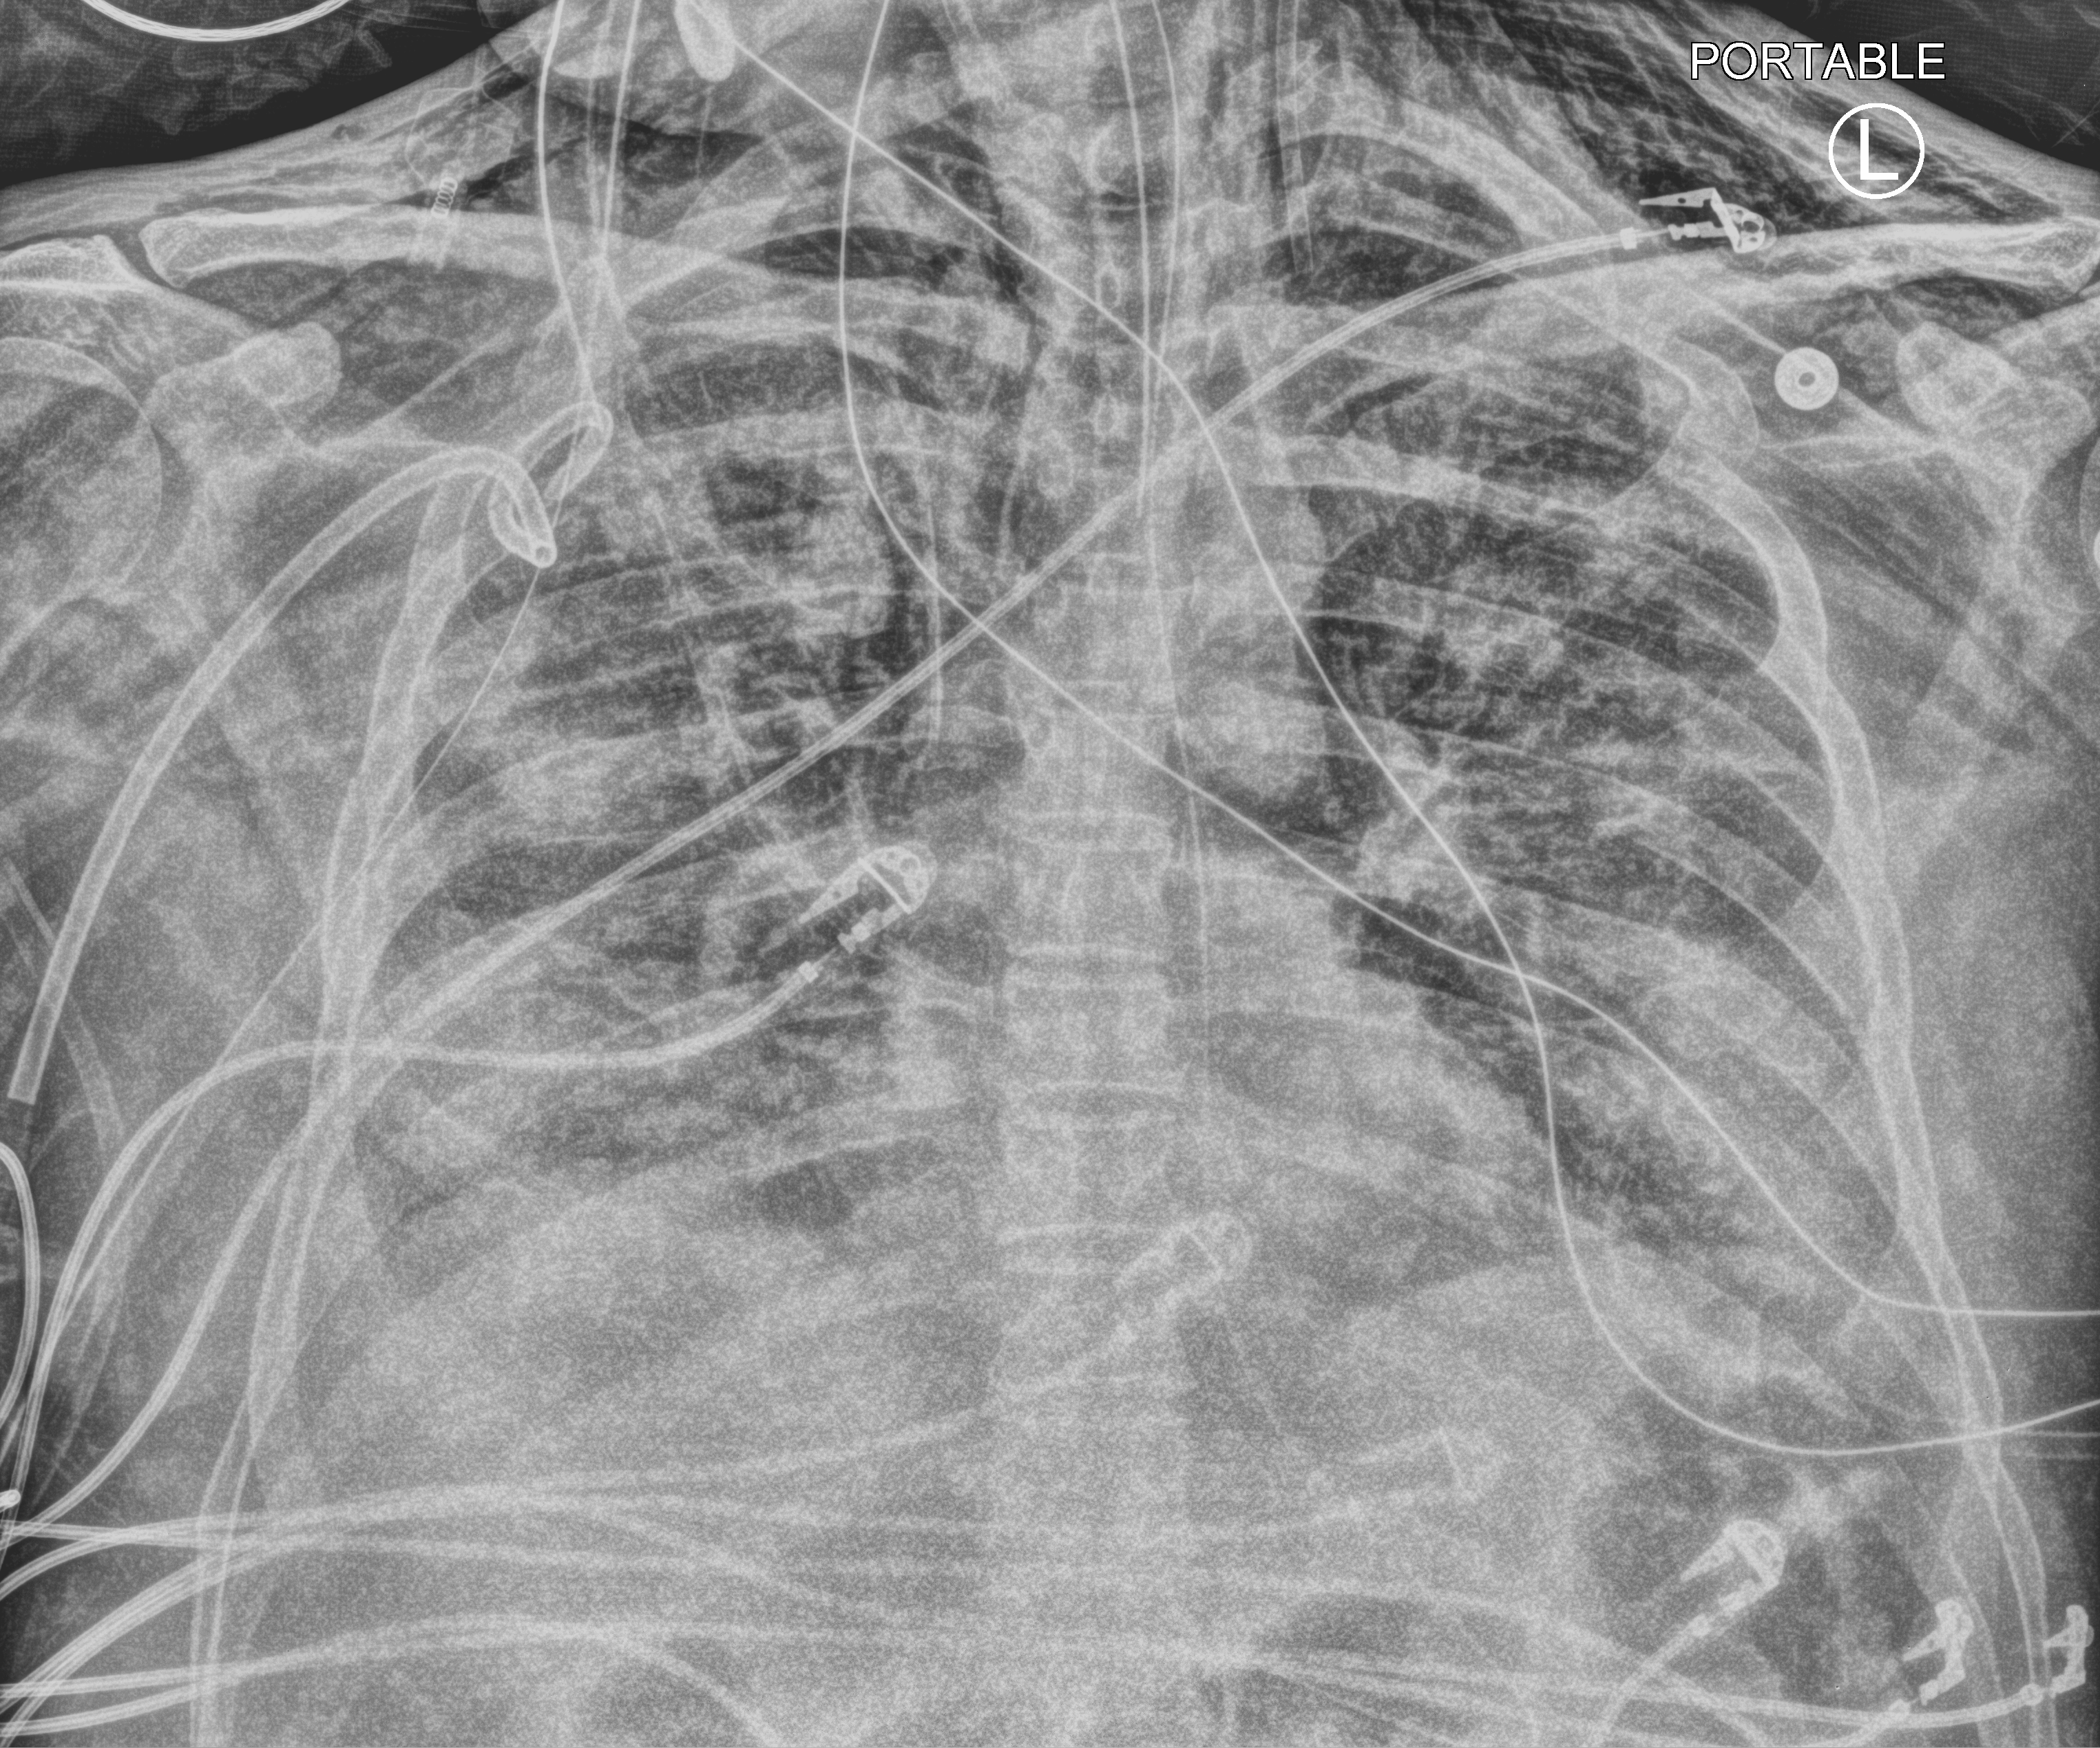
Portable chest radiograph, anteroposterior (AP) projection. Male patient hospitalised with COVID-19, age 60–74 years.
Hospital-stay facts (about this admission, not read from this image; timing relative to this image not recorded):
- admitted to intensive care during this hospital stay: yes
- mechanically ventilated during this hospital stay: yes